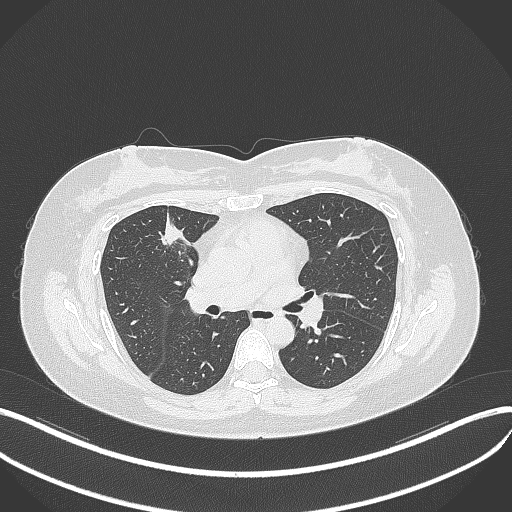
Chest CT, one axial slice; position 179 of 273 along the scan axis; reconstruction kernel B70f; 120 kVp; lung window (W 1500 / L -600 HU); 1 mm slice thickness; 512 × 512 image matrix, field of view 400 × 400 mm. Patient: female, 42 years. Case-level facts recorded for this patient, not image findings: clinical TNM (as recorded): T1b N0 M0.
Structures marked on this image (rectangle marked by the reading radiologist):
- lung tumour (recorded histology: adenocarcinoma): bounding box <157,212,191,250> (left, top, right, bottom; pixels)